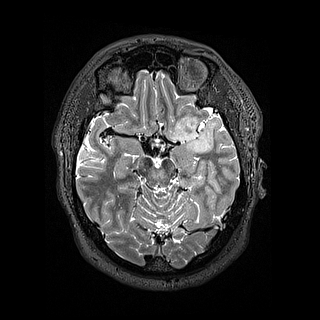
Brain MRI from a brain-tumour surgery series, one axial slice; slice 98 of 144 in the series (ordered by position); 1.2 mm slice thickness; 320 × 320 image matrix. Case-level facts recorded for this patient, not image findings: histopathology: Astrocytoma; WHO grade: 2; IDH mutation: yes.
Structures marked on this image (outlined manually by an expert reader):
- tumour: box from (x=171, y=113) to (x=204, y=154) px